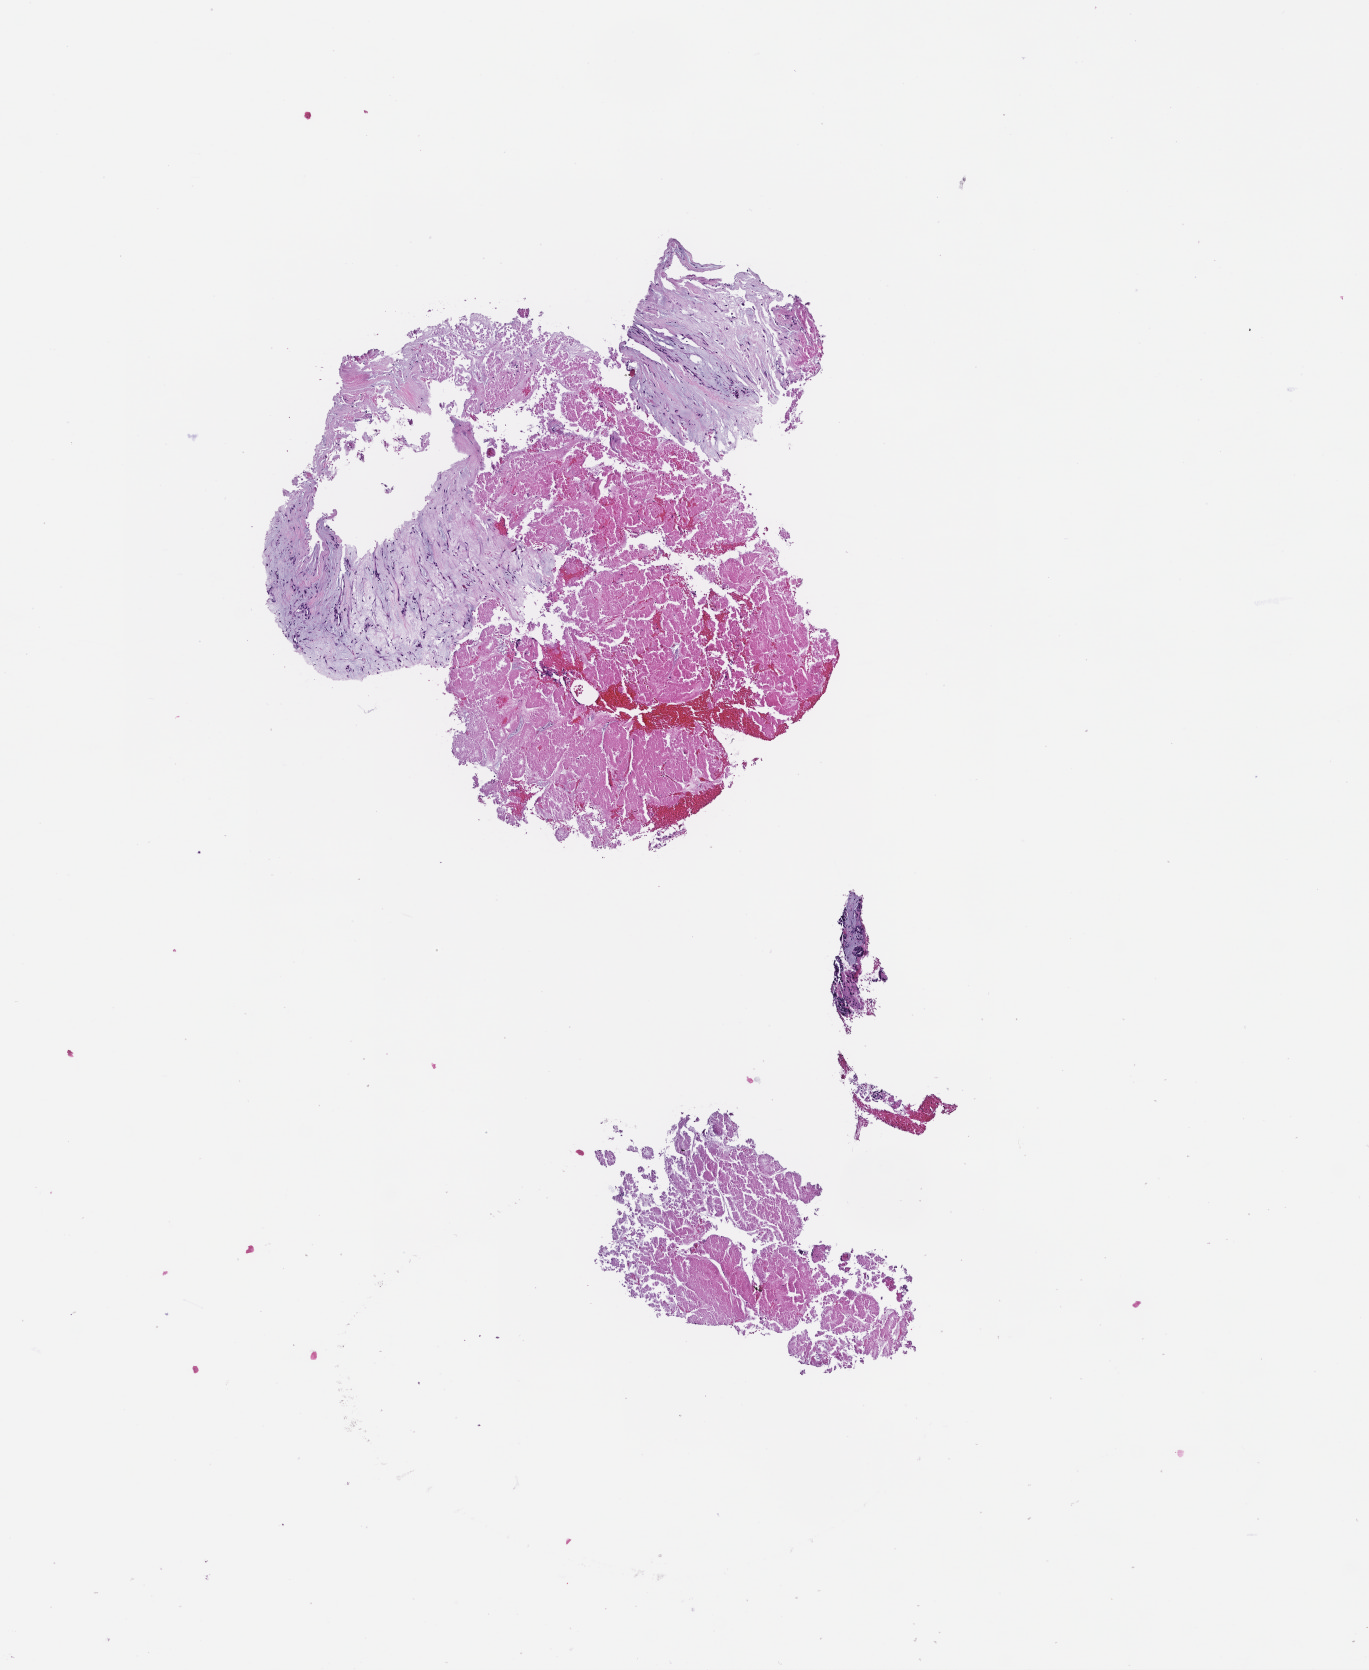
Digitized haematoxylin and eosin-stained section, shown as a low-resolution overview of the whole scanned area (about 5.5 x 6.7 mm). Formalin-fixed, paraffin-embedded (FFPE) tissue. Specimen time point: archival tissue. Male patient.
This section: metastatic tumor tissue. Primary diagnosis of the patient: Prostate Carcinoma.